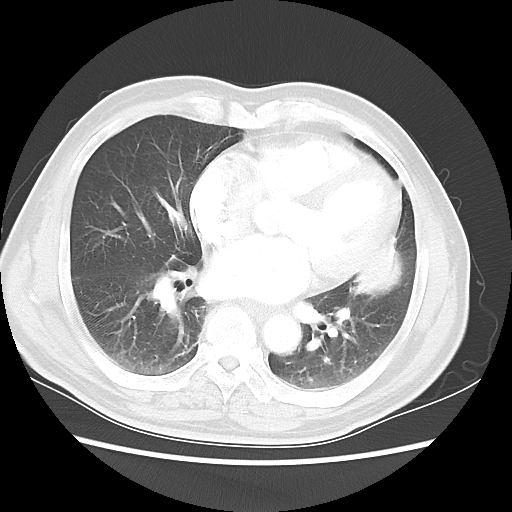
Chest CT, one axial slice. Slice 20 of 50 in the series (ordered by position). 120 kVp. Lung window (W 1500 / L -600 HU). 5 mm slice thickness. 512 × 512 image matrix, field of view 360 × 360 mm. Patient: male, 69 years. Case-level facts recorded for this patient, not image findings: clinical TNM (as recorded): T3 N1 M1a.
Annotated regions visible in this slice (rectangle marked by the reading radiologist):
- lung tumour (recorded histology: squamous cell carcinoma): box from (x=351, y=241) to (x=417, y=305) px